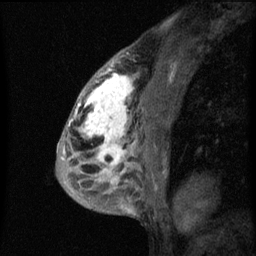
Breast MRI (dynamic contrast-enhanced), one sagittal slice. Slice 35 of 60 in the series (ordered by position). Dynamic contrast-enhanced series, image 2 of 3 at this slice position (ordered by acquisition). 1.5 T. TE 4.2 ms, TR 8 ms. 2 mm slice thickness. 256 × 256 image matrix. Patient: female, 50 years.
Structures marked on this image (semi-automatically segmented with operator editing):
- analysis volume of interest (the breast-tissue region the enhancement analysis was run in; not a lesion): bounding box <66,64,141,187> (left, top, right, bottom; pixels)
- tumour enhancement mask (voxels above the 70 % enhancement threshold inside the analysis volume of interest): <68,64,133,183>